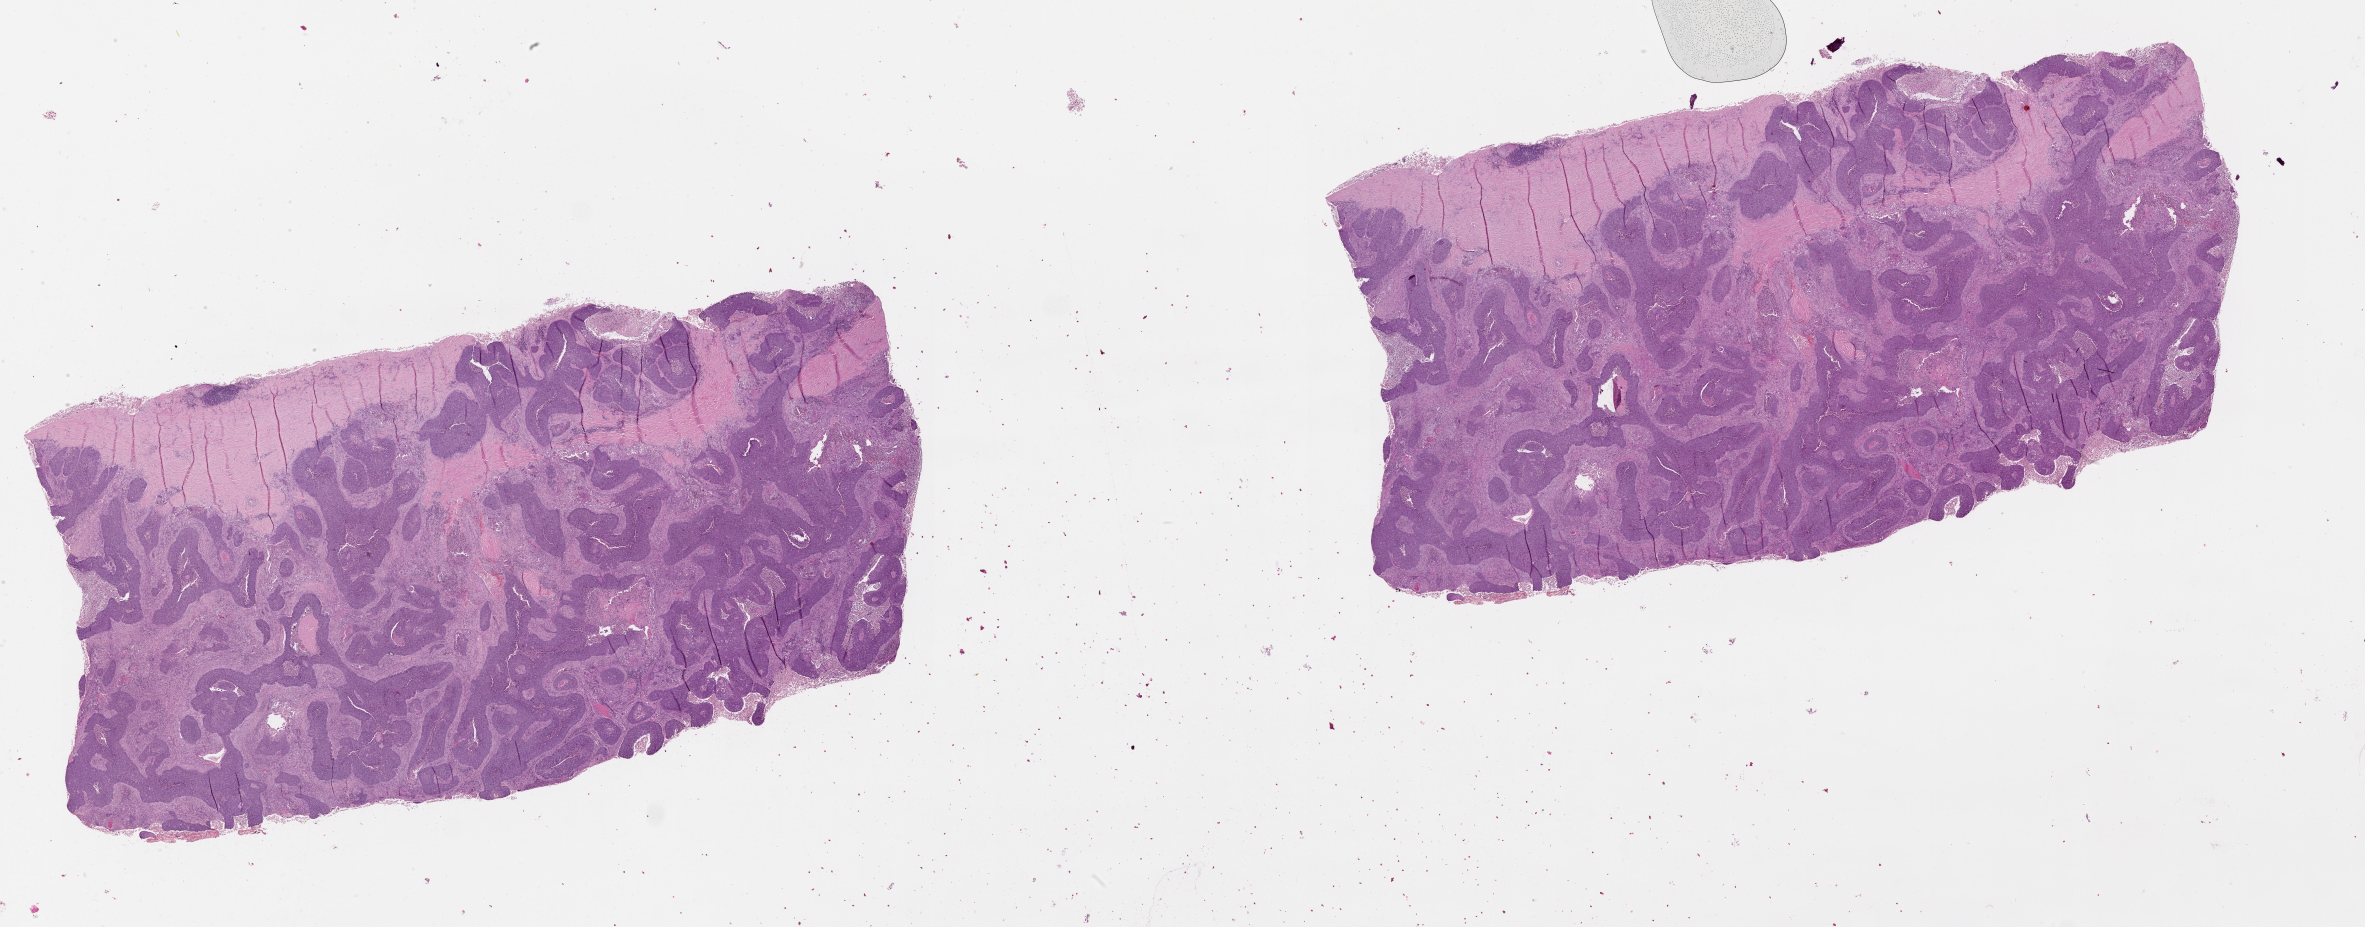
Whole-slide histology image, H&E-stained — whole scanned area (about 38.1 x 14.9 mm) shown as a low-resolution overview, tumour tissue sample, lung. Patient: male, age 69 years.
- patient diagnosis (cohort enrolment): squamous cell carcinoma (lung)